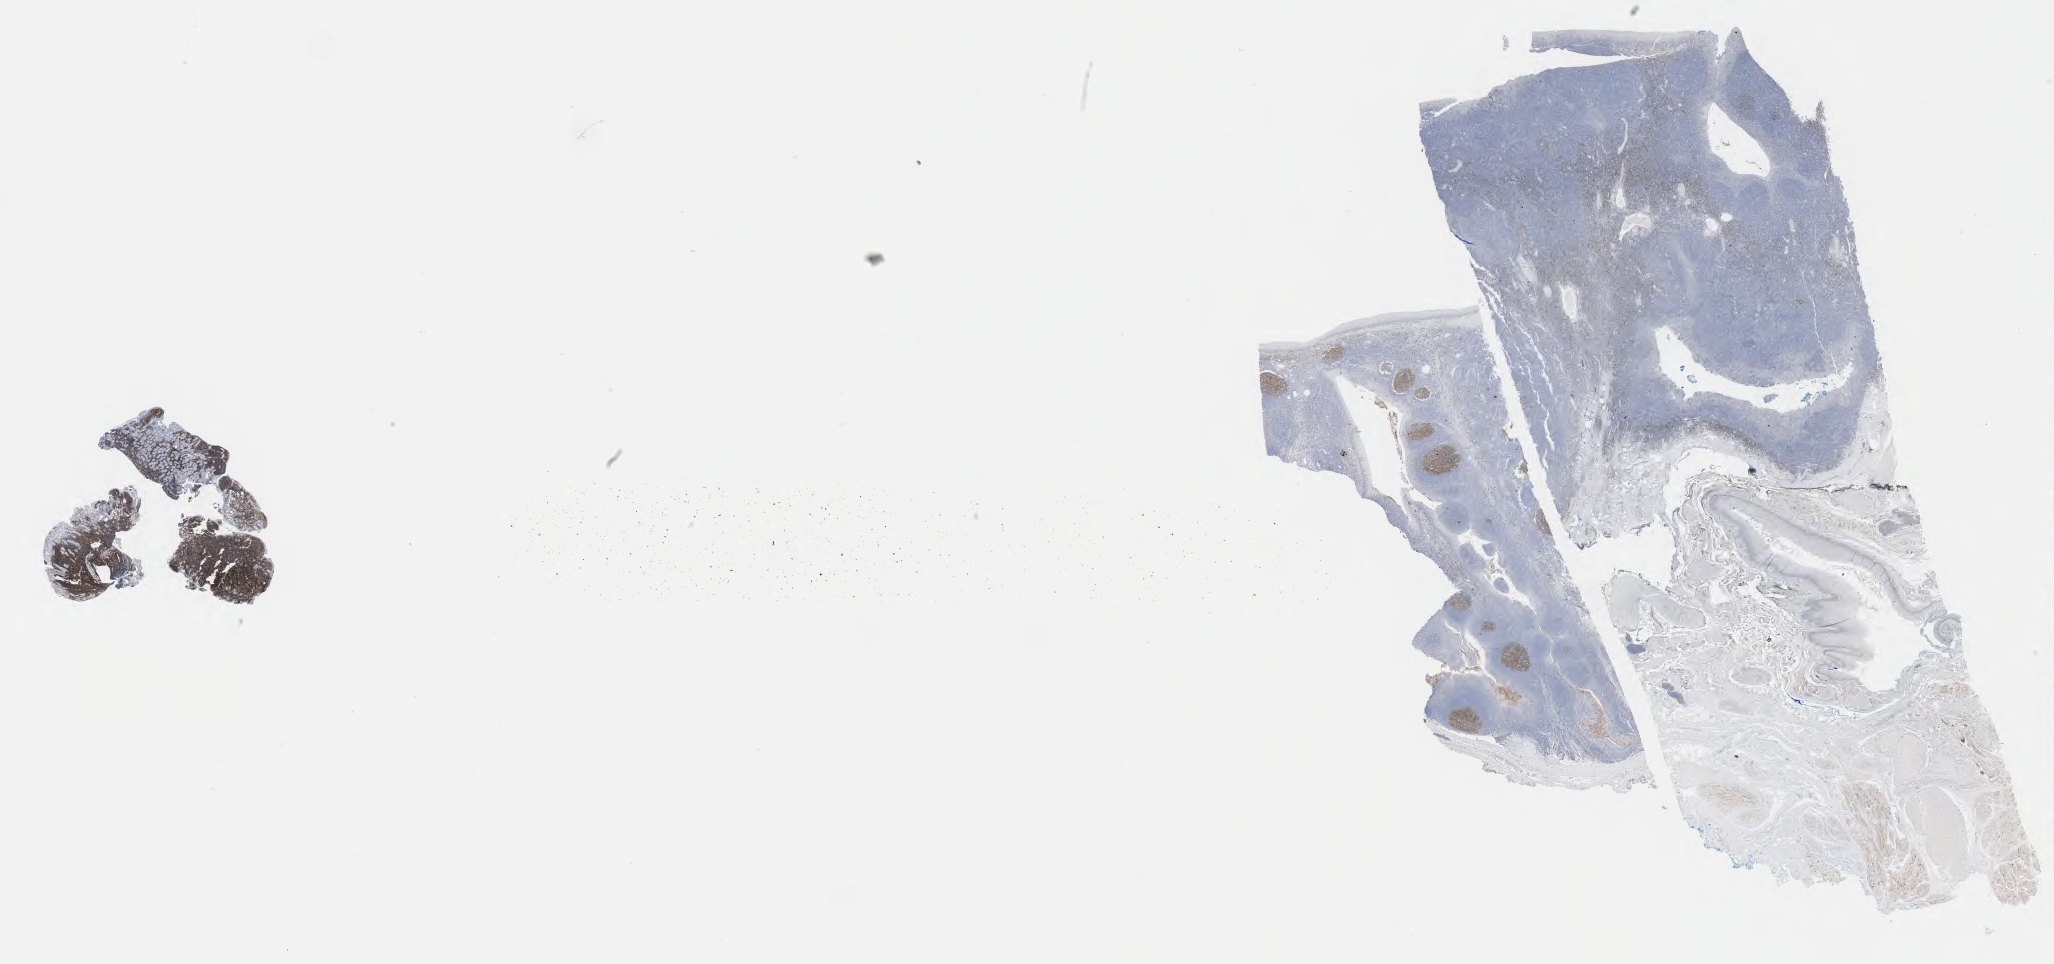
Immunohistochemistry (IHC) whole-slide image stained for CD10 — a low-resolution overview of the entire scanned area, about 33.2 x 15.6 mm, tumor tissue. Patient female; age 45 years.
Diagnosis: Burkitt lymphoma, NOS.